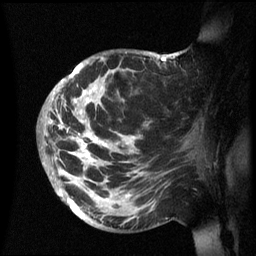
Breast MRI (dynamic contrast-enhanced), one sagittal slice. Slice 39 of 60 in the series (ordered by position). Dynamic contrast-enhanced series, image 2 of 3 at this slice position (ordered by acquisition). 1.5 T. TE 4.2 ms, TR 8.4 ms. 2.4 mm slice thickness. 256 × 256 image matrix. Patient: female, 48 years.
Structures marked on this image (semi-automatic segmentation, software-assisted and operator-edited):
- analysis volume of interest (the breast-tissue region the enhancement analysis was run in; not a lesion): bounding box (x1, y1, x2, y2) in pixels: (42, 52, 202, 236)
- tumour enhancement mask (voxels above the 70 % enhancement threshold inside the analysis volume of interest): (43, 54, 179, 204)